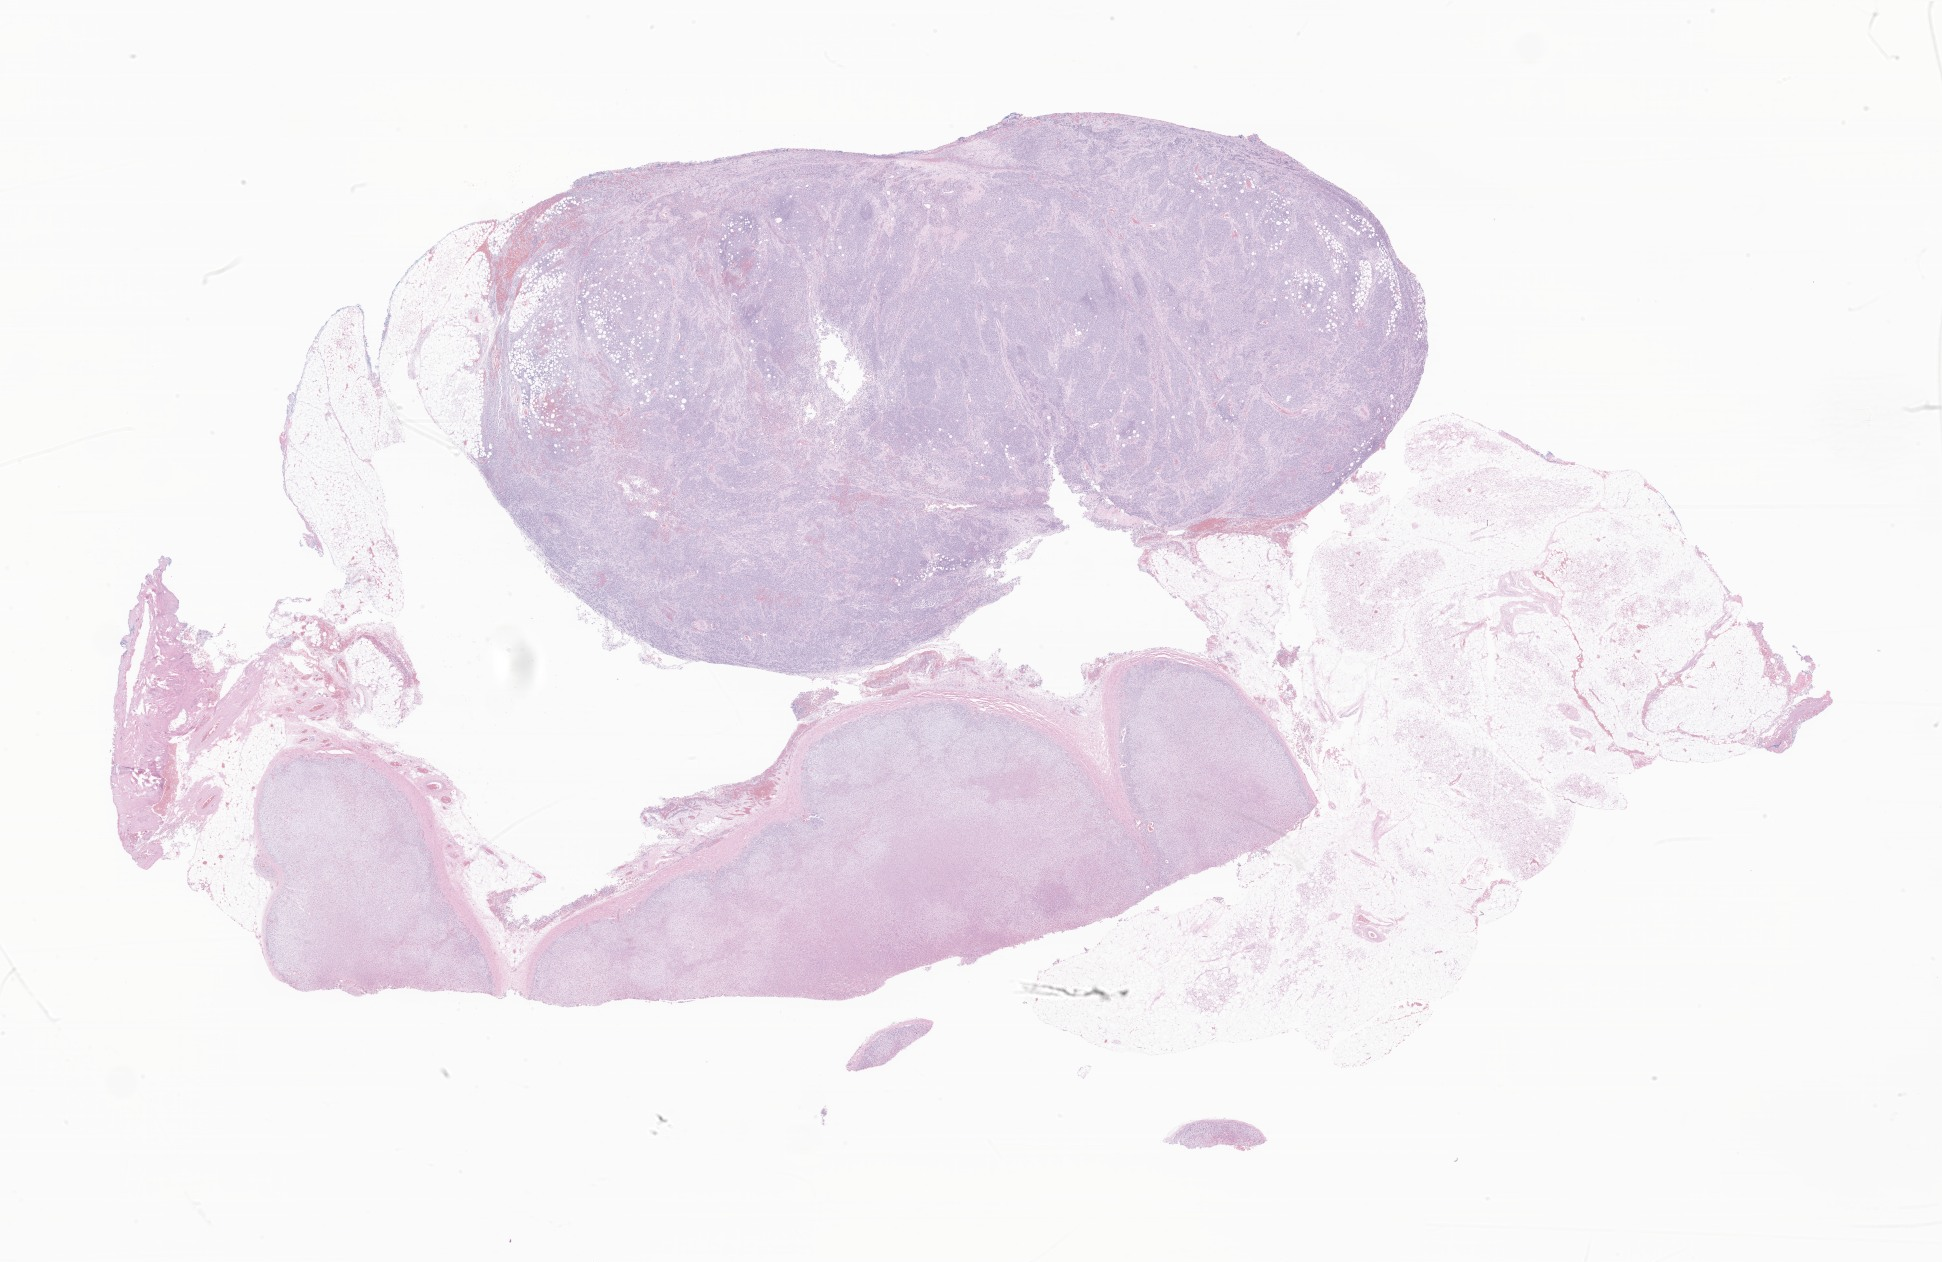
Digitized haematoxylin and eosin-stained section of tumor tissue from the soft tissue of lower extremity, whole scanned area (about 32.8 x 21.3 mm) shown as a low-resolution overview, FFPE section. Male patient, age 214 months (17 years 10 months).
Recorded diagnosis: Alveolar rhabdomyosarcoma.